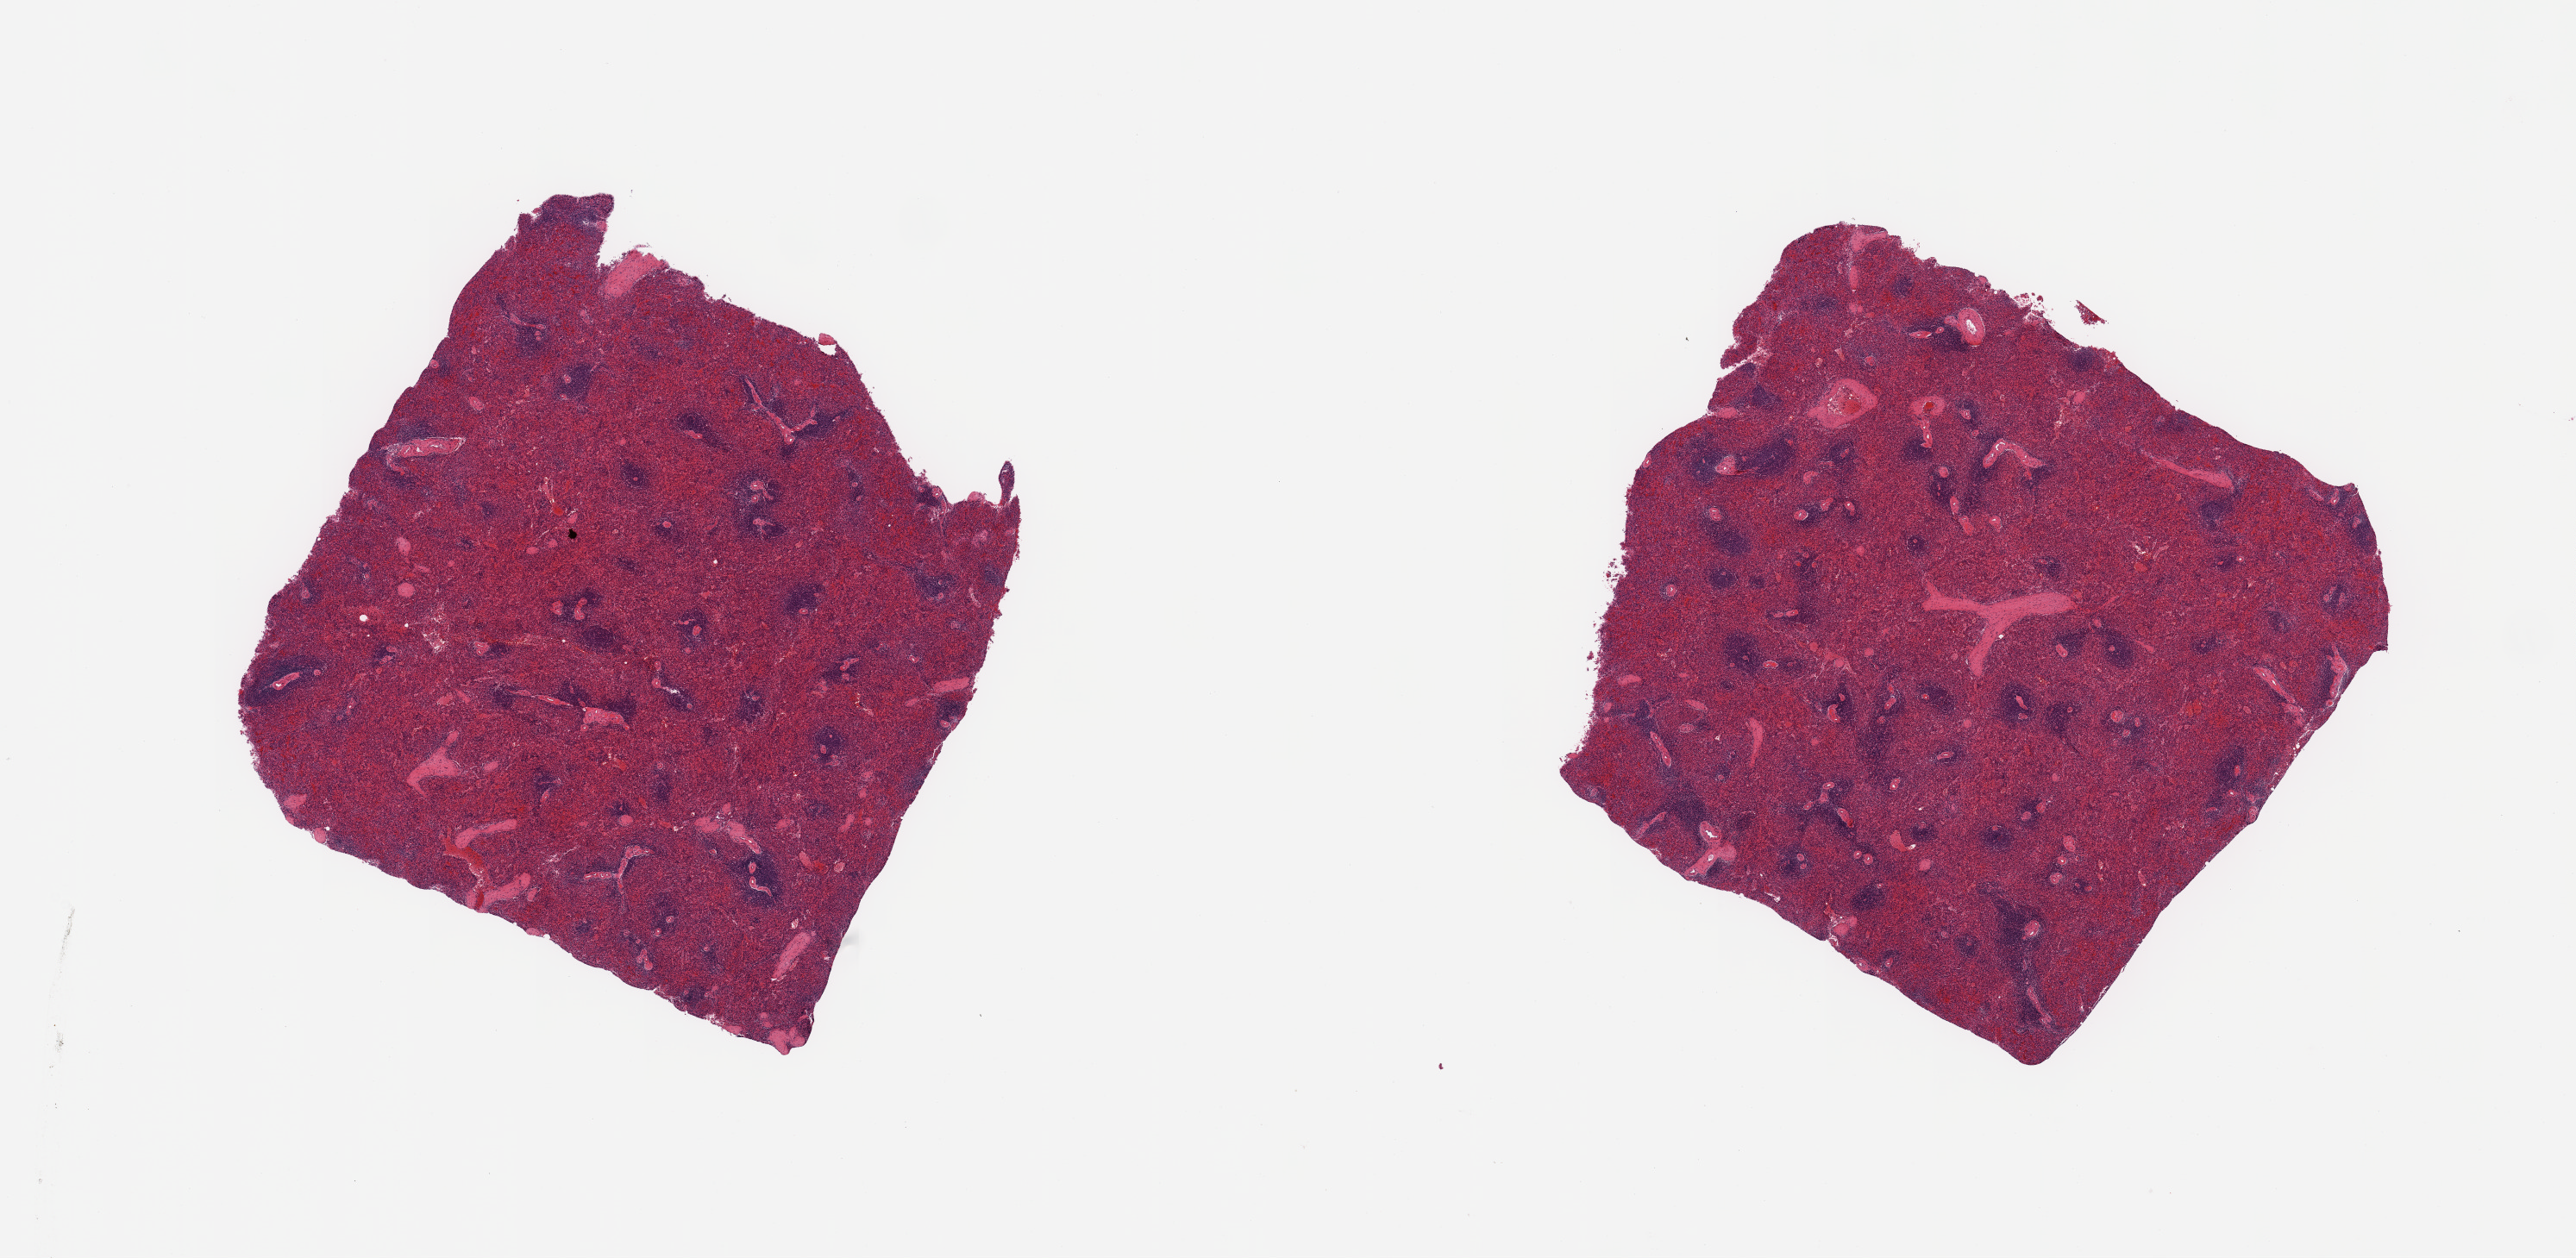
Digitized haematoxylin and eosin-stained section — shown as a low-resolution overview of the whole scanned area (about 23.6 x 11.5 mm); PAXgene-fixed, paraffin-embedded tissue; section of spleen (target tissue); donor tissue sample. Donor sex: female.
Review note (as recorded): 2 pieces, no abnormalities.